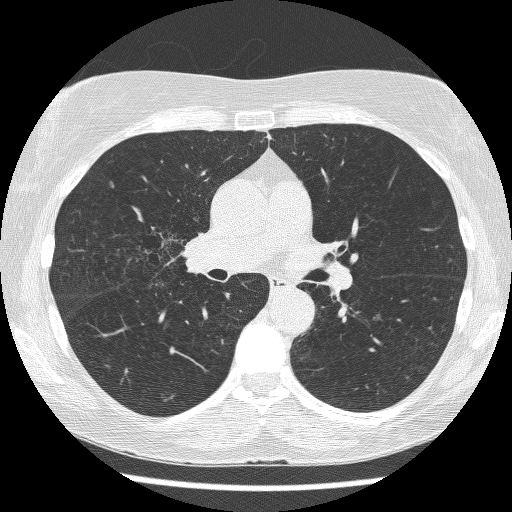
Axial slice from a low-dose chest CT screening exam, baseline screening round, lung window (W 1500 / L -600 HU), 1.25 mm slice thickness, lung (sharp) reconstruction kernel (BONE), 512 × 512 image matrix. Female participant, aged 64 years at enrolment. Former smoker at enrolment.
- Lesion marked by an expert reader, box from (x=121, y=212) to (x=196, y=269) px.
- The screening reader recorded 3 non-calcified nodules or masses ≥4 mm on this exam (right upper lobe, right upper lobe, left lower lobe); which of them this box marks is not recorded.